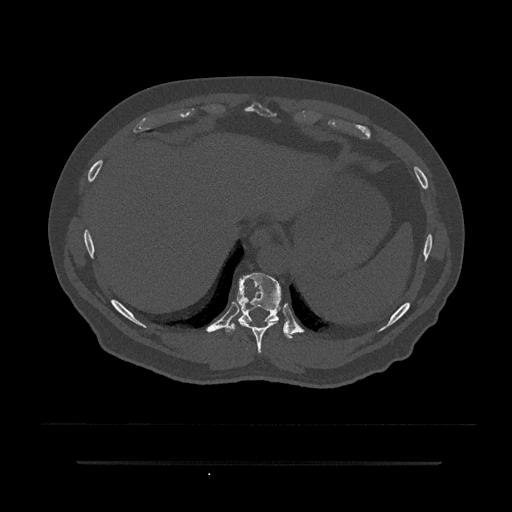
CT including the spine, one axial slice. Position 351 of 797 along the scan axis. 120 kVp. Bone window (W 1800 / L 400 HU). 0.5 mm slice thickness. 512 × 512 image matrix. Male patient, age 59 years. From the clinical record (not read from this slice): primary cancer: bile ducts.
Annotated regions visible in this slice (semi-automatic segmentation, software-assisted and operator-edited):
- T10 vertebra: bounding box (x1, y1, x2, y2) in pixels: (226, 273, 293, 339)
- T9 vertebra: (241, 323, 274, 353)